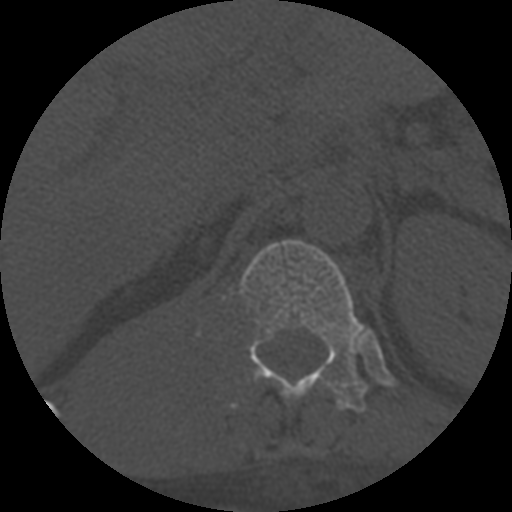
CT including the spine, one axial slice; position 316 of 708 along the scan axis; one of 3 acquisitions stored at this slice position; bone window (W 1800 / L 400 HU); 512 × 512 image matrix. Patient age 55 years. From the clinical record (not read from this slice): primary cancer: colon.
Outlined on this slice (semi-automatically segmented with operator editing):
- T12 vertebra: box from (x=238, y=239) to (x=367, y=412) px